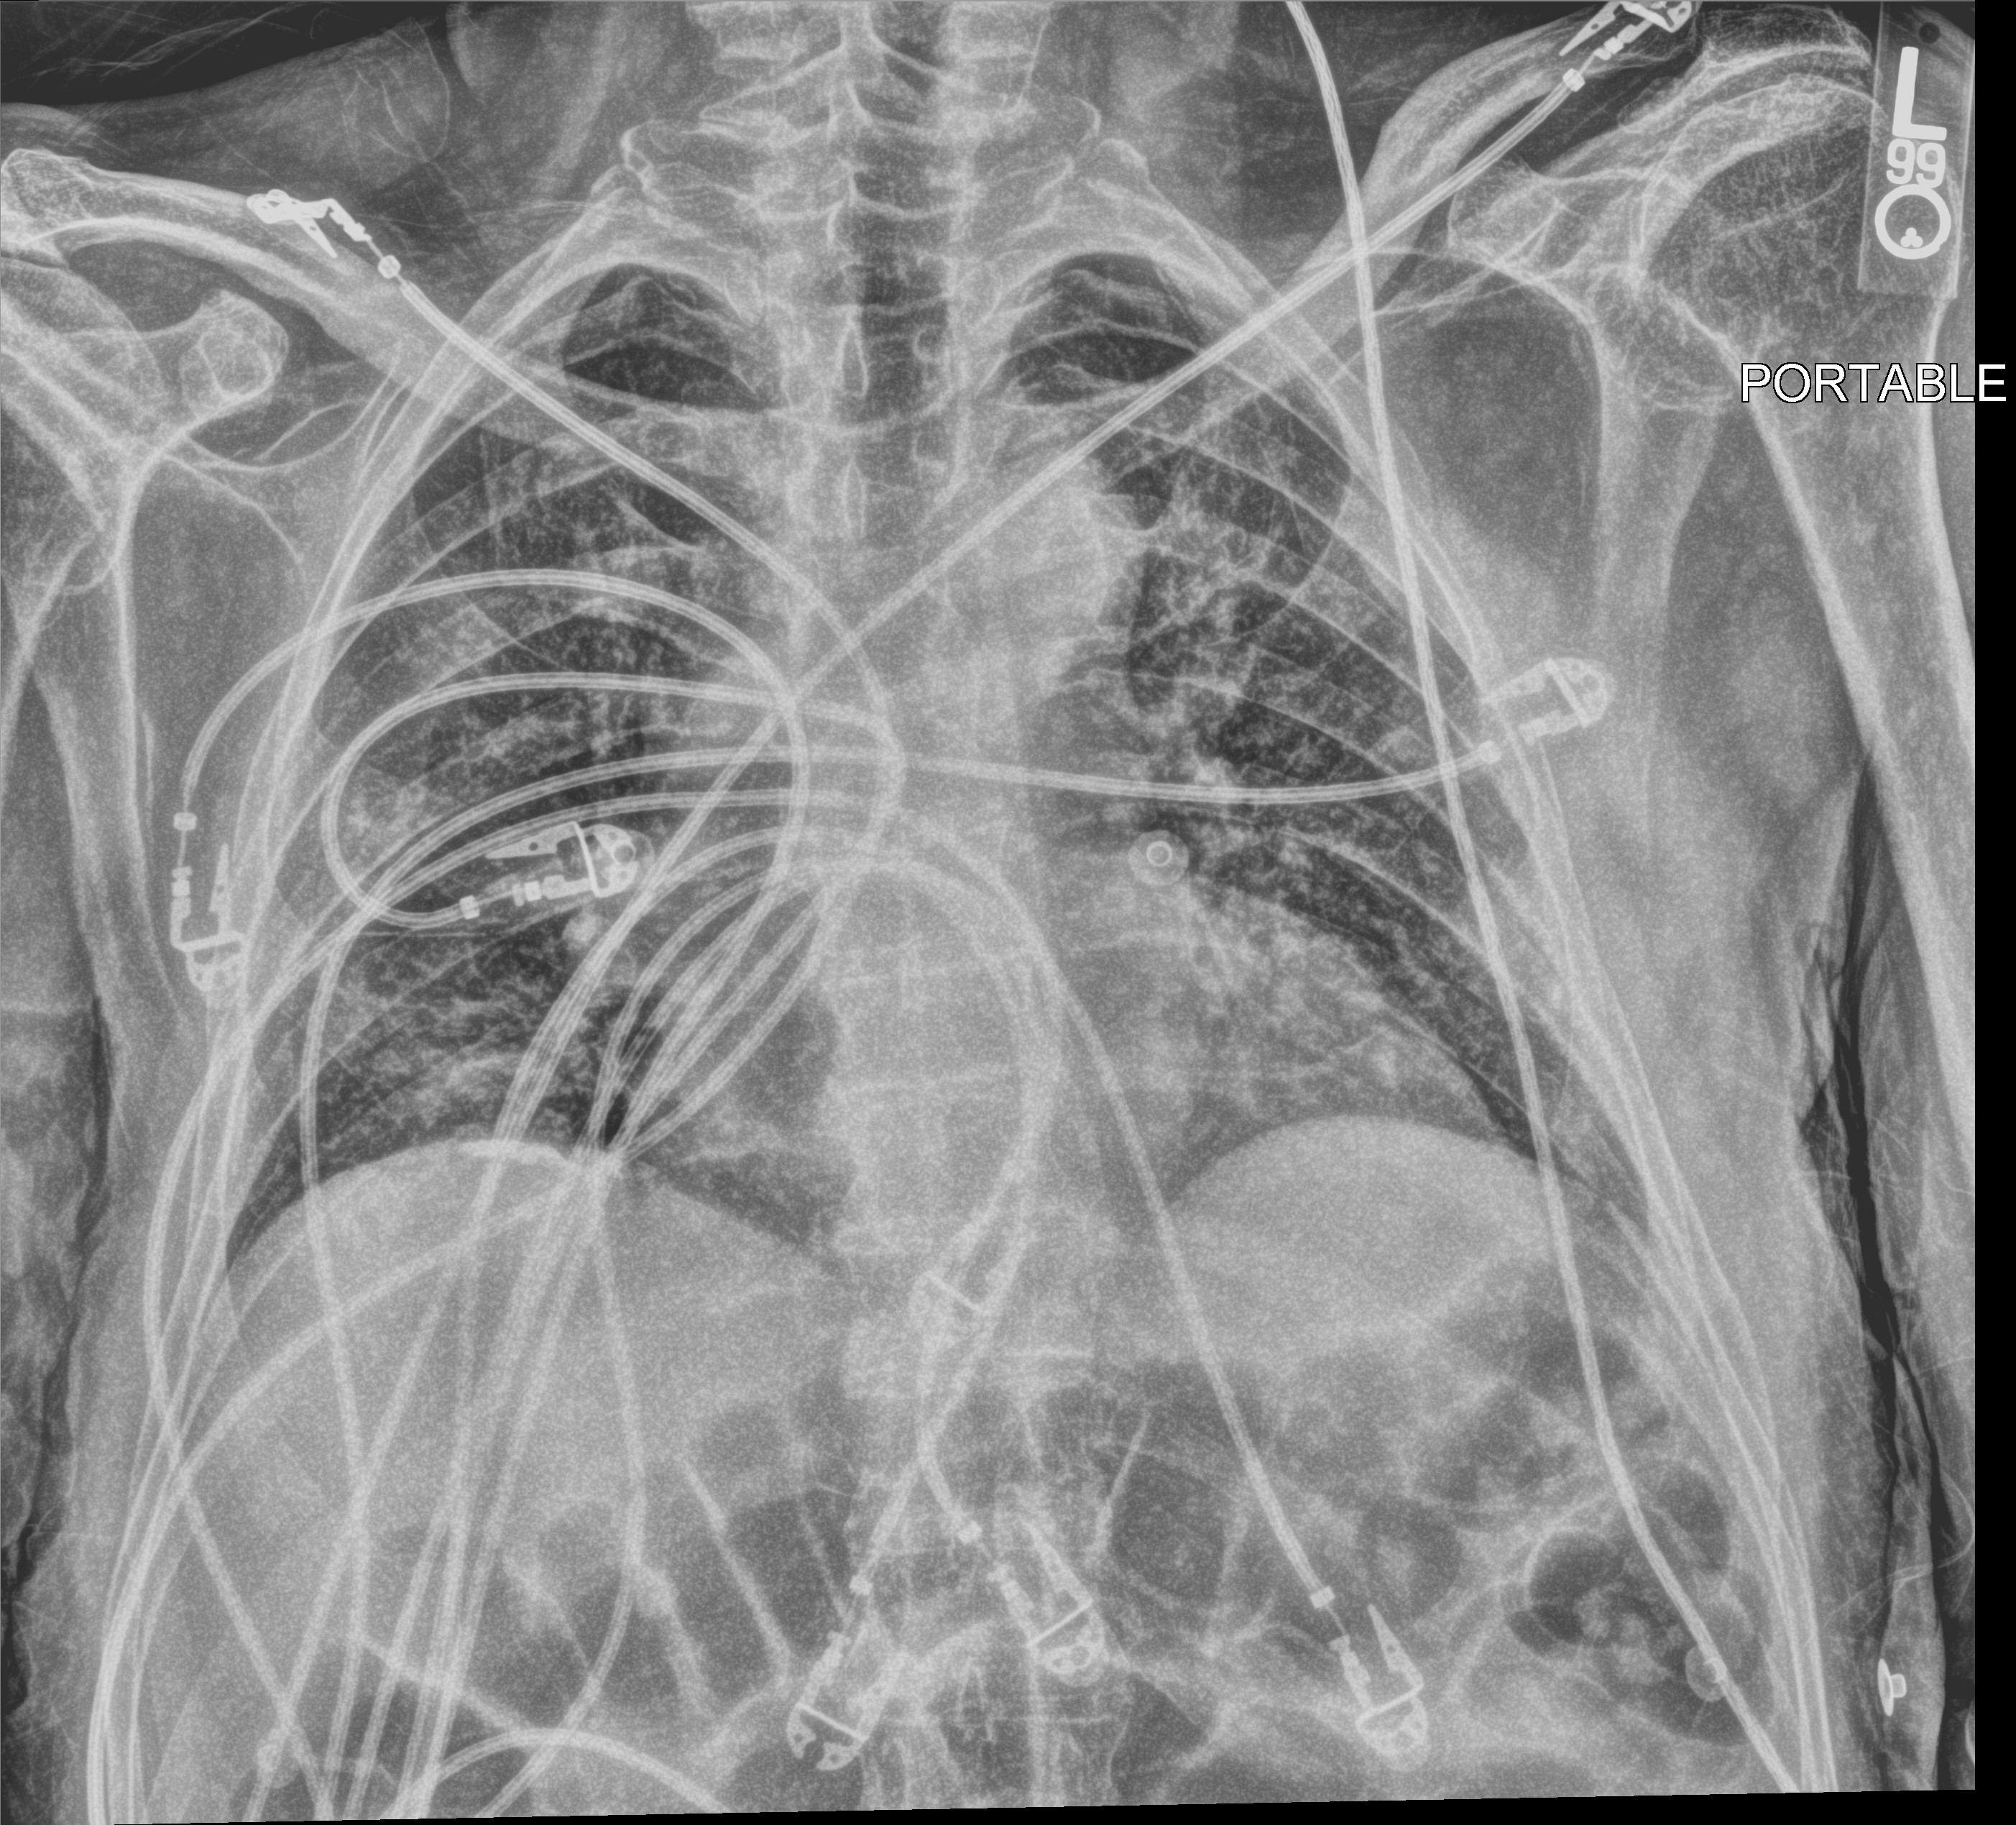
Bedside chest radiograph (computed radiography). Patient hospitalised with COVID-19; male, aged 75–90 years.
Admission-level facts for this patient (not findings on this image; timing relative to this image not recorded): mechanically ventilated during this hospital stay: no; admitted to intensive care during this hospital stay: no.